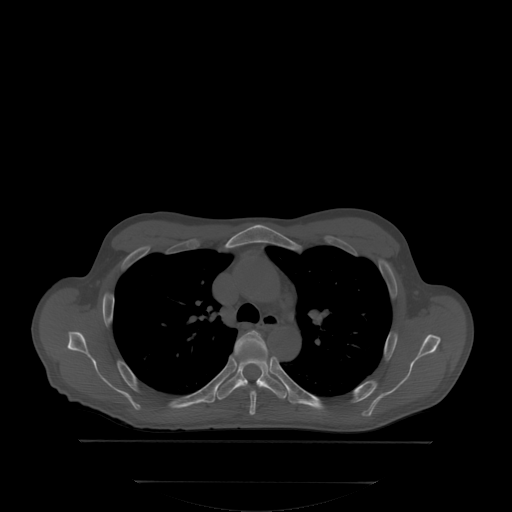
CT including the spine, one axial slice. Bone window (W 1800 / L 400 HU). 512 × 512 image matrix, field of view 500 × 500 mm. Male patient, age 58 years. Case-level facts recorded for this patient, not image findings: primary cancer: prostate; vertebrae with lytic lesions (as recorded): L1.
Annotated regions visible in this slice (semi-automatic segmentation, software-assisted and operator-edited):
- T4 vertebra: box from (x=234, y=331) to (x=267, y=414) px
- T5 vertebra: (x=216, y=357)–(x=288, y=399)